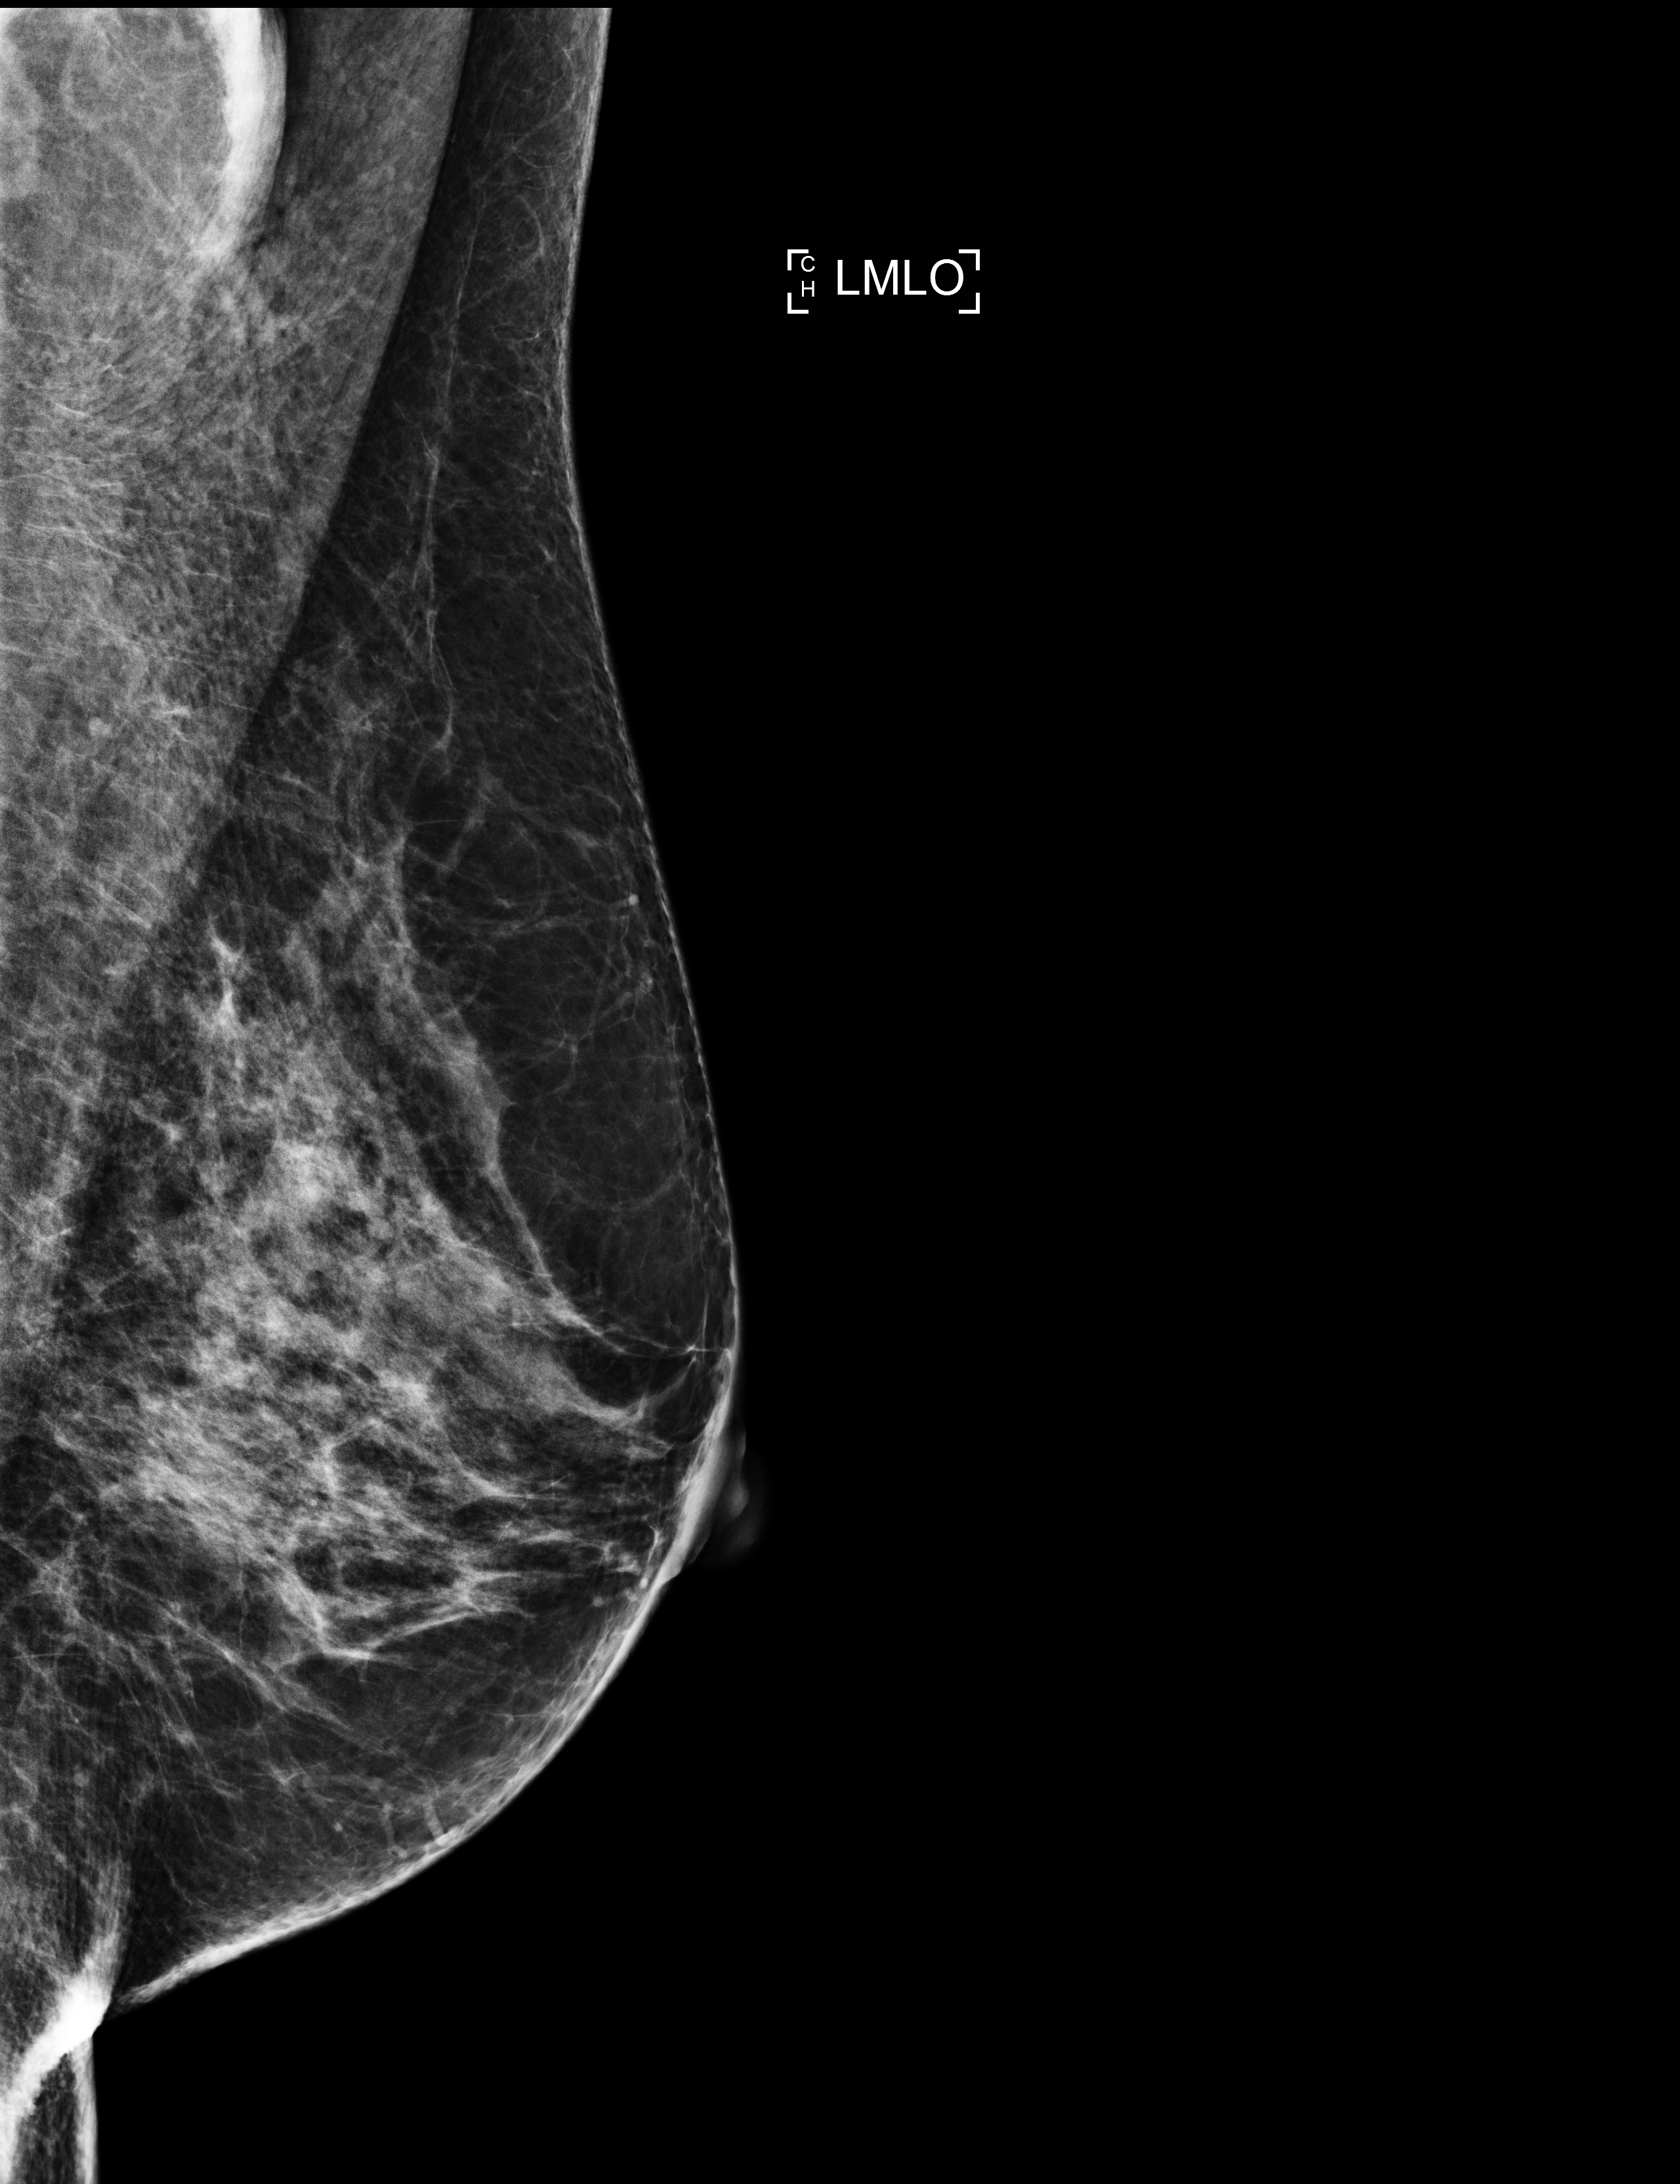
Screening examination, compressed breast thickness 64 mm. Female patient, age 60 years.
Image type: full-field digital mammogram. Breast: left. Projection: mediolateral oblique (MLO) view.